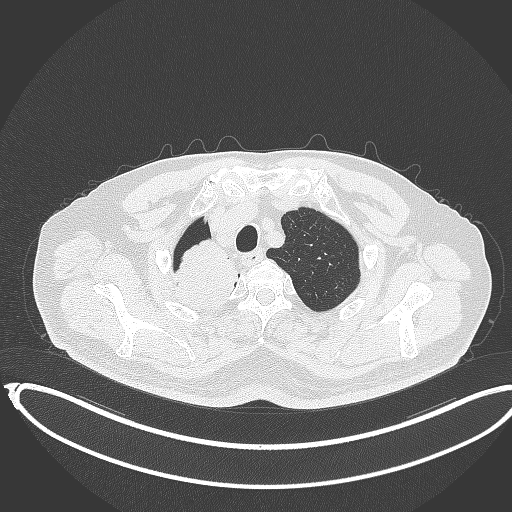
Chest CT, one axial slice. Position 322 of 403 along the scan axis. Reconstruction kernel B70f. Lung window (W 1500 / L -600 HU). 1 mm slice thickness. 512 × 512 image matrix, field of view 436 × 436 mm. Male patient, age 68 years. From the clinical record (not read from this slice): clinical TNM (as recorded): T2a N0 M0.
Structures marked on this image (bounding box drawn by a radiologist):
- lung tumour (recorded histology: adenocarcinoma): bounding box <168,238,241,313> (left, top, right, bottom; pixels)